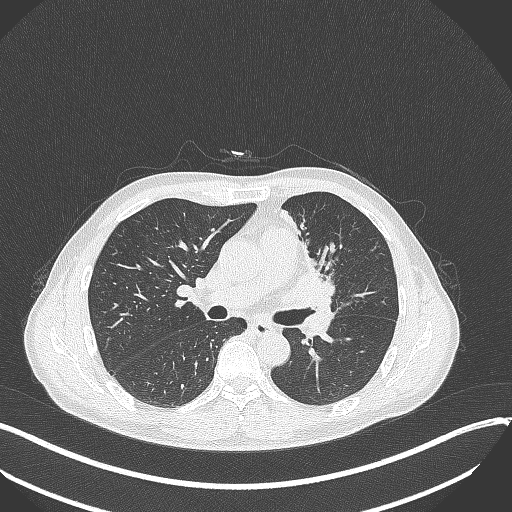
Chest CT, one axial slice. Slice 191 of 411 in the series (ordered by position). Reconstruction kernel B70f. 120 kVp. Lung window (W 1500 / L -600 HU). 1 mm slice thickness. 512 × 512 image matrix, field of view 400 × 400 mm. Male patient, age 56 years. From the clinical record (not read from this slice): clinical TNM (as recorded): T2a N0 M0.
Structures marked on this image (bounding box drawn by a radiologist):
- lung tumour (recorded histology: squamous cell carcinoma): bounding box [x1, y1, x2, y2] px = [279, 266, 336, 311]